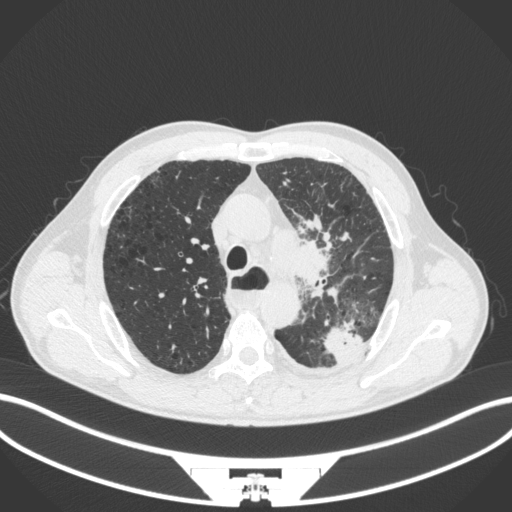
Chest CT, one axial slice. Position 280 of 411 along the scan axis. Reconstruction kernel B31f. 120 kVp. Lung window (W 1500 / L -600 HU). 512 × 512 image matrix, field of view 400 × 400 mm. Male patient, age 57 years. Case-level facts recorded for this patient, not image findings: clinical TNM (as recorded): T2a N1 M0.
Outlined on this slice (rectangle marked by the reading radiologist):
- lung tumour (recorded histology: squamous cell carcinoma): bounding box <291,232,340,299> (left, top, right, bottom; pixels)